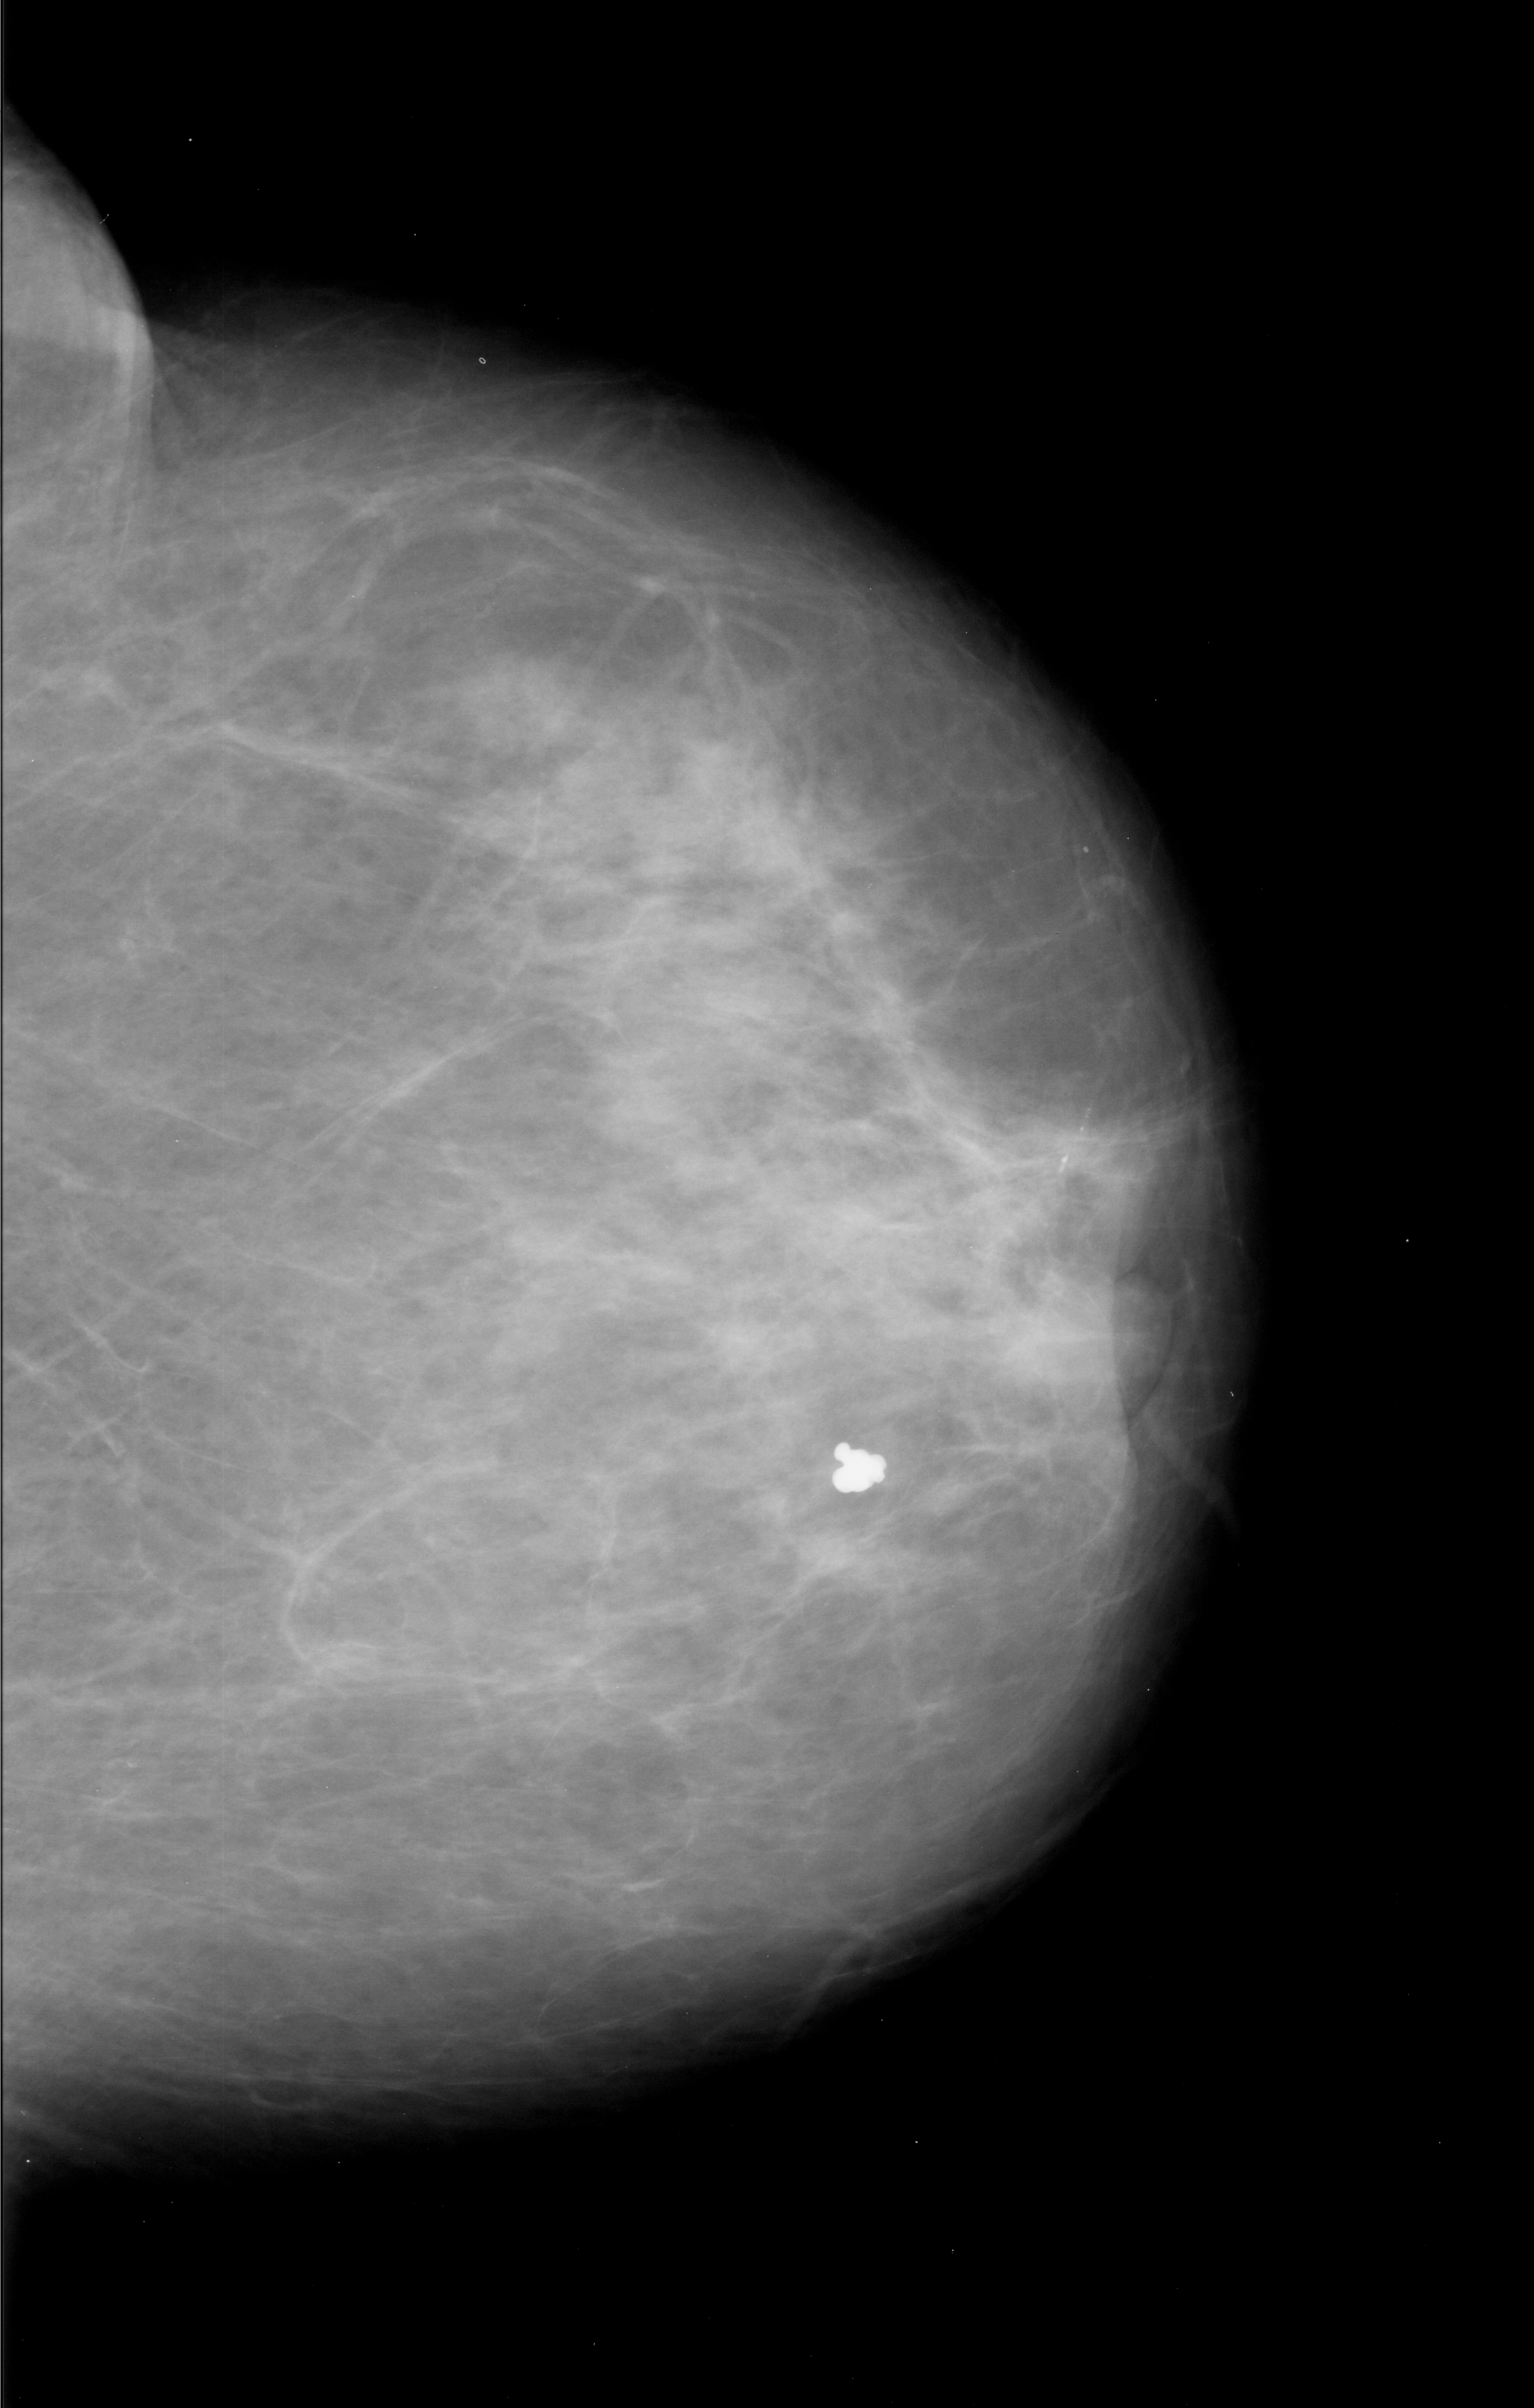
Scanned film-screen mammogram. Right breast. CC view. 1534 × 2408 image matrix.
Marked abnormalities (boxes around the expert regions of interest):
- calcifications, morphology pleomorphic, distribution linear; BI-RADS assessment category 4; subtlety rating 4 on a 1 (subtle) to 5 (obvious) scale; pathology (as recorded): malignant: bounding box <1041,1083,1102,1193> (left, top, right, bottom; pixels)